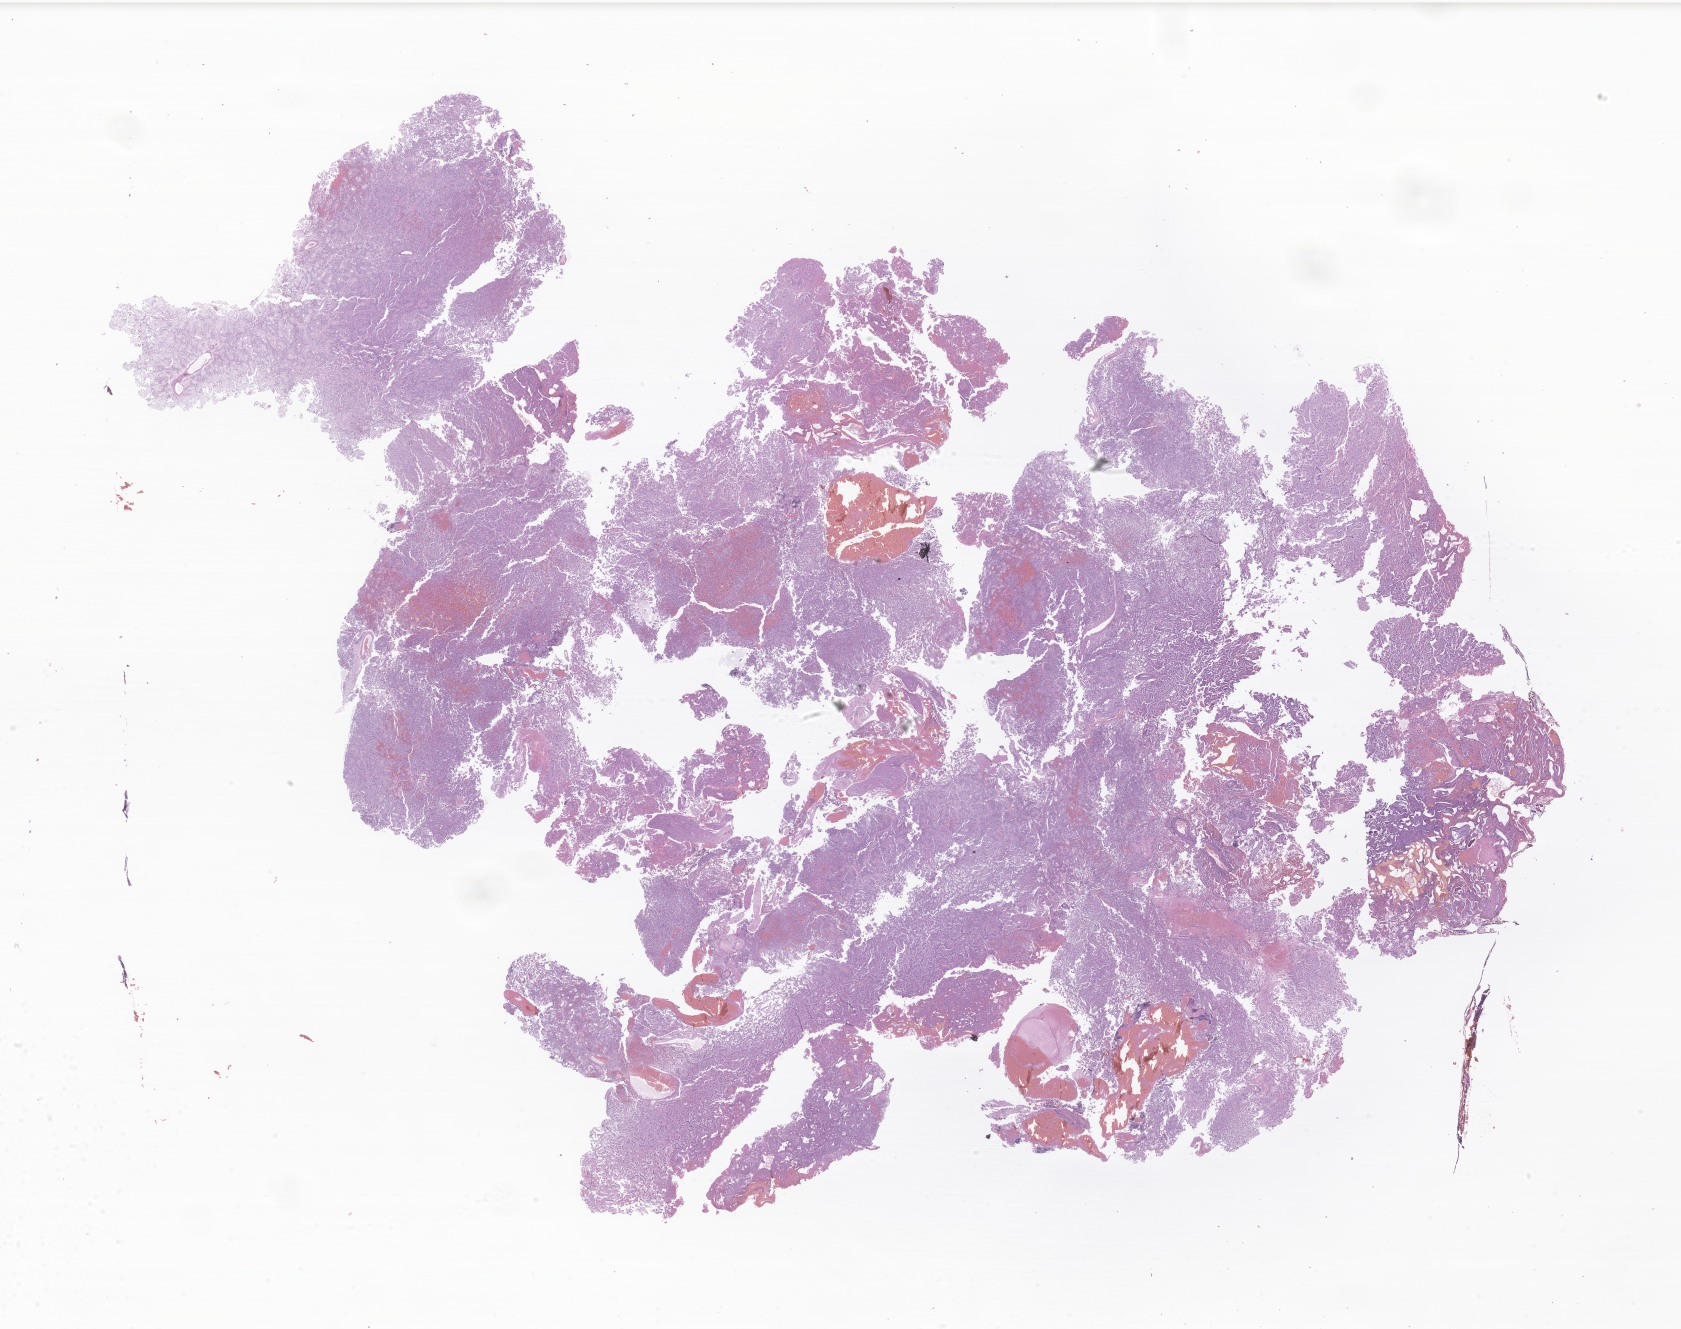
H&E whole-slide image of tumor tissue from the brain — whole scanned area (about 28.4 x 22.4 mm) shown as a low-resolution overview. Formalin-fixed, paraffin-embedded (FFPE) tissue. Patient: female, age 82 months (6 years 10 months).
* diagnosis: Glioma, malignant